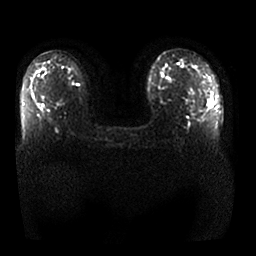
Breast MRI, one axial slice; position 14 of 25 along the scan axis; diffusion-weighted series; image 2 of 4 stored at this slice position (different b-values; order by instance number); 1.5 T; 4 mm slice thickness; 256 × 256 image matrix, field of view 360 × 360 mm. Female patient.
Annotated regions visible in this slice (expert manual segmentation):
- tumour on diffusion-weighted imaging: bounding box [x1, y1, x2, y2] px = [208, 99, 212, 107]